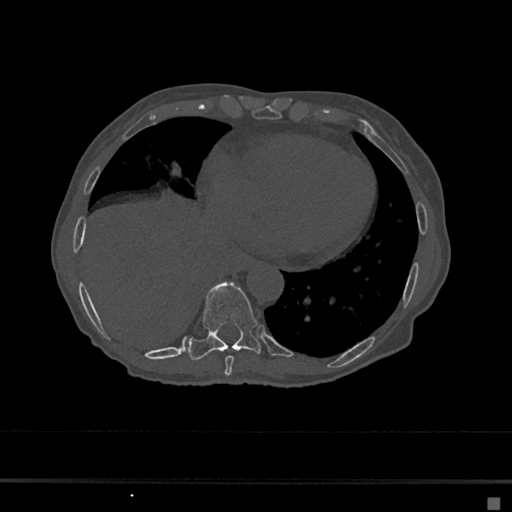
CT including the spine, one axial slice. Slice 281 of 797 in the series (ordered by position). 120 kVp. Bone window (W 1800 / L 400 HU). 0.5 mm slice thickness. 512 × 512 image matrix. Female patient, age 68 years. Case-level facts recorded for this patient, not image findings: primary cancer: renal.
Outlined on this slice (semi-automatic segmentation, software-assisted and operator-edited):
- T8 vertebra: bounding box <225,355,234,376> (left, top, right, bottom; pixels)
- T9 vertebra: <189,283,261,360>